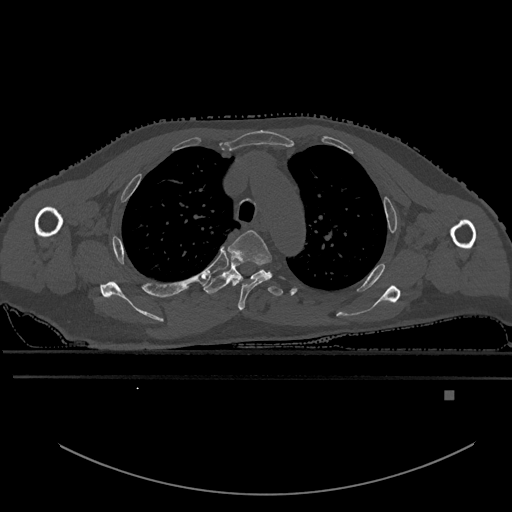
CT including the spine, one axial slice; slice 430 of 969 in the series (ordered by position); bone window (W 1800 / L 400 HU); 512 × 512 image matrix. Male patient, age 82 years. Case-level facts recorded for this patient, not image findings: primary cancer: prostate; vertebrae with lytic lesions (as recorded): T11, T9, T8, T2.
Structures marked on this image (semi-automatic segmentation, software-assisted and operator-edited):
- T3 vertebra: bounding box [x1, y1, x2, y2] px = [228, 230, 272, 311]
- T4 vertebra: [203, 262, 283, 297]